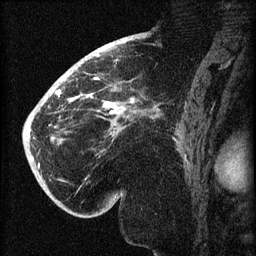
Breast MRI (dynamic contrast-enhanced), one sagittal slice; slice 44 of 60 in the series (ordered by position); dynamic contrast-enhanced series, image 2 of 3 at this slice position (ordered by acquisition); 1.5 T; TE 4.2 ms, TR 8.2 ms; 2 mm slice thickness; 256 × 256 image matrix, field of view 180 × 180 mm. Patient: female, 71 years.
Structures marked on this image (semi-automatic segmentation, software-assisted and operator-edited):
- analysis volume of interest (the breast-tissue region the enhancement analysis was run in; not a lesion): bounding box <40,72,148,196> (left, top, right, bottom; pixels)
- tumour enhancement mask (voxels above the 70 % enhancement threshold inside the analysis volume of interest): <56,77,134,114>